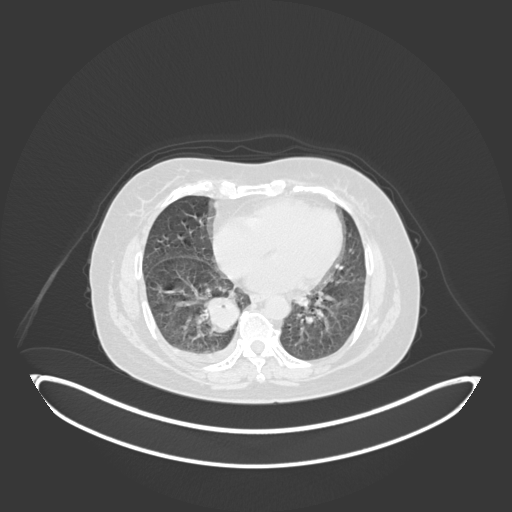
Chest CT, one axial slice. Position 58 of 231 along the scan axis. Lung window (W 1500 / L -600 HU). 1 mm slice thickness. 512 × 512 image matrix. Female patient, age 56 years. Case-level facts recorded for this patient, not image findings: clinical TNM (as recorded): T2b N1 M0; histopathological grade: G3.
Annotated regions visible in this slice (rectangle marked by the reading radiologist):
- lung tumour (recorded histology: small cell carcinoma): bounding box <206,293,244,334> (left, top, right, bottom; pixels)